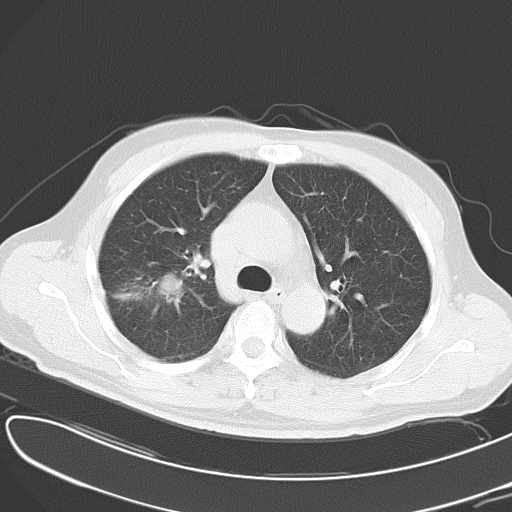
Chest CT, one axial slice; slice 34 of 49 in the series (ordered by position); reconstruction kernel B70f; 120 kVp; lung window (W 1500 / L -600 HU); 512 × 512 image matrix, field of view 353 × 353 mm. Patient: male, 53 years. Case-level facts recorded for this patient, not image findings: clinical TNM (as recorded): T2 N1 M0.
Outlined on this slice (rectangle marked by the reading radiologist):
- lung tumour (recorded histology: adenocarcinoma): bounding box [x1, y1, x2, y2] px = [114, 265, 194, 315]